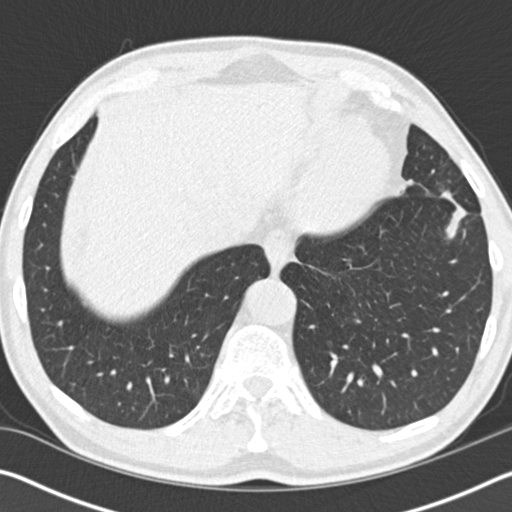
Low-dose screening chest CT, one axial slice. Position 35 of 162 along the scan axis. 120 kVp. Lung window (W 1500 / L -600 HU). 2 mm slice thickness. 512 × 512 image matrix, field of view 340 × 340 mm.
Annotated regions visible in this slice (expert manual segmentation):
- lesion 1 (tumor, upper lobe of left lung): bounding box (x1, y1, x2, y2) in pixels: (445, 205, 467, 239)